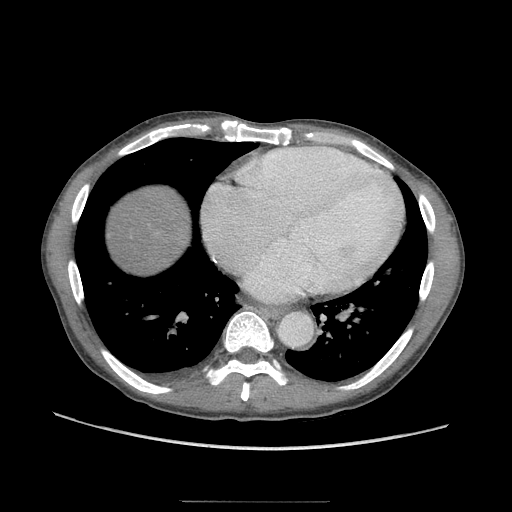
Contrast-enhanced abdominal CT (liver protocol), one axial slice. Position 99 of 103 along the scan axis. 120 kVp. Soft-tissue window (W 400 / L 40 HU). 2.5 mm slice thickness. 512 × 512 image matrix. From the clinical record (not read from this slice): diagnosis: hepatocellular carcinoma (patient treated with transarterial chemoembolisation; whether this scan precedes or follows treatment is not stated here); TNM stage (as recorded): Stage-IIIA; Child-Pugh class: A; tumour nodularity: multinodular; tumour size: 16 cm.
Annotated regions visible in this slice (semi-automatically segmented with operator editing):
- abdominal aorta: bounding box (x1, y1, x2, y2) in pixels: (278, 311, 311, 345)
- liver parenchyma outside the tumour (the mass and vessels are separate outlines, so this box may not span the whole liver): (114, 192, 180, 264)